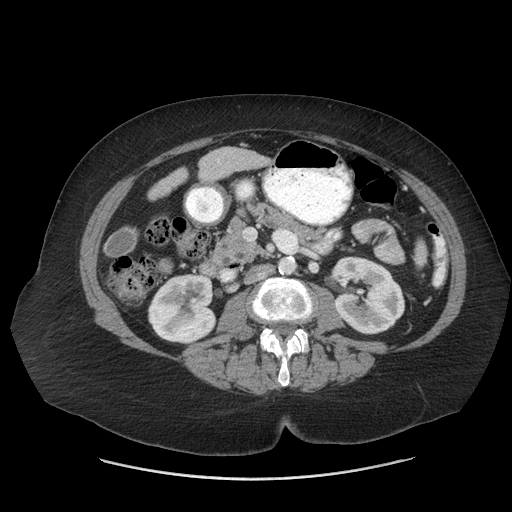
Contrast-enhanced abdominal CT (liver protocol), one axial slice; position 14 of 69 along the scan axis; reconstruction kernel STANDARD; 140 kVp; soft-tissue window (W 400 / L 40 HU); 512 × 512 image matrix, field of view 420 × 420 mm. From the clinical record (not read from this slice): diagnosis: hepatocellular carcinoma (patient treated with transarterial chemoembolisation; whether this scan precedes or follows treatment is not stated here); TNM stage (as recorded): Stage-IIIB; Child-Pugh class: A; tumour differentiation: moderately differentiated.
Outlined on this slice (semi-automatic segmentation, software-assisted and operator-edited):
- liver parenchyma outside the tumour (the mass and vessels are separate outlines, so this box may not span the whole liver): bounding box [x1, y1, x2, y2] px = [198, 146, 266, 182]